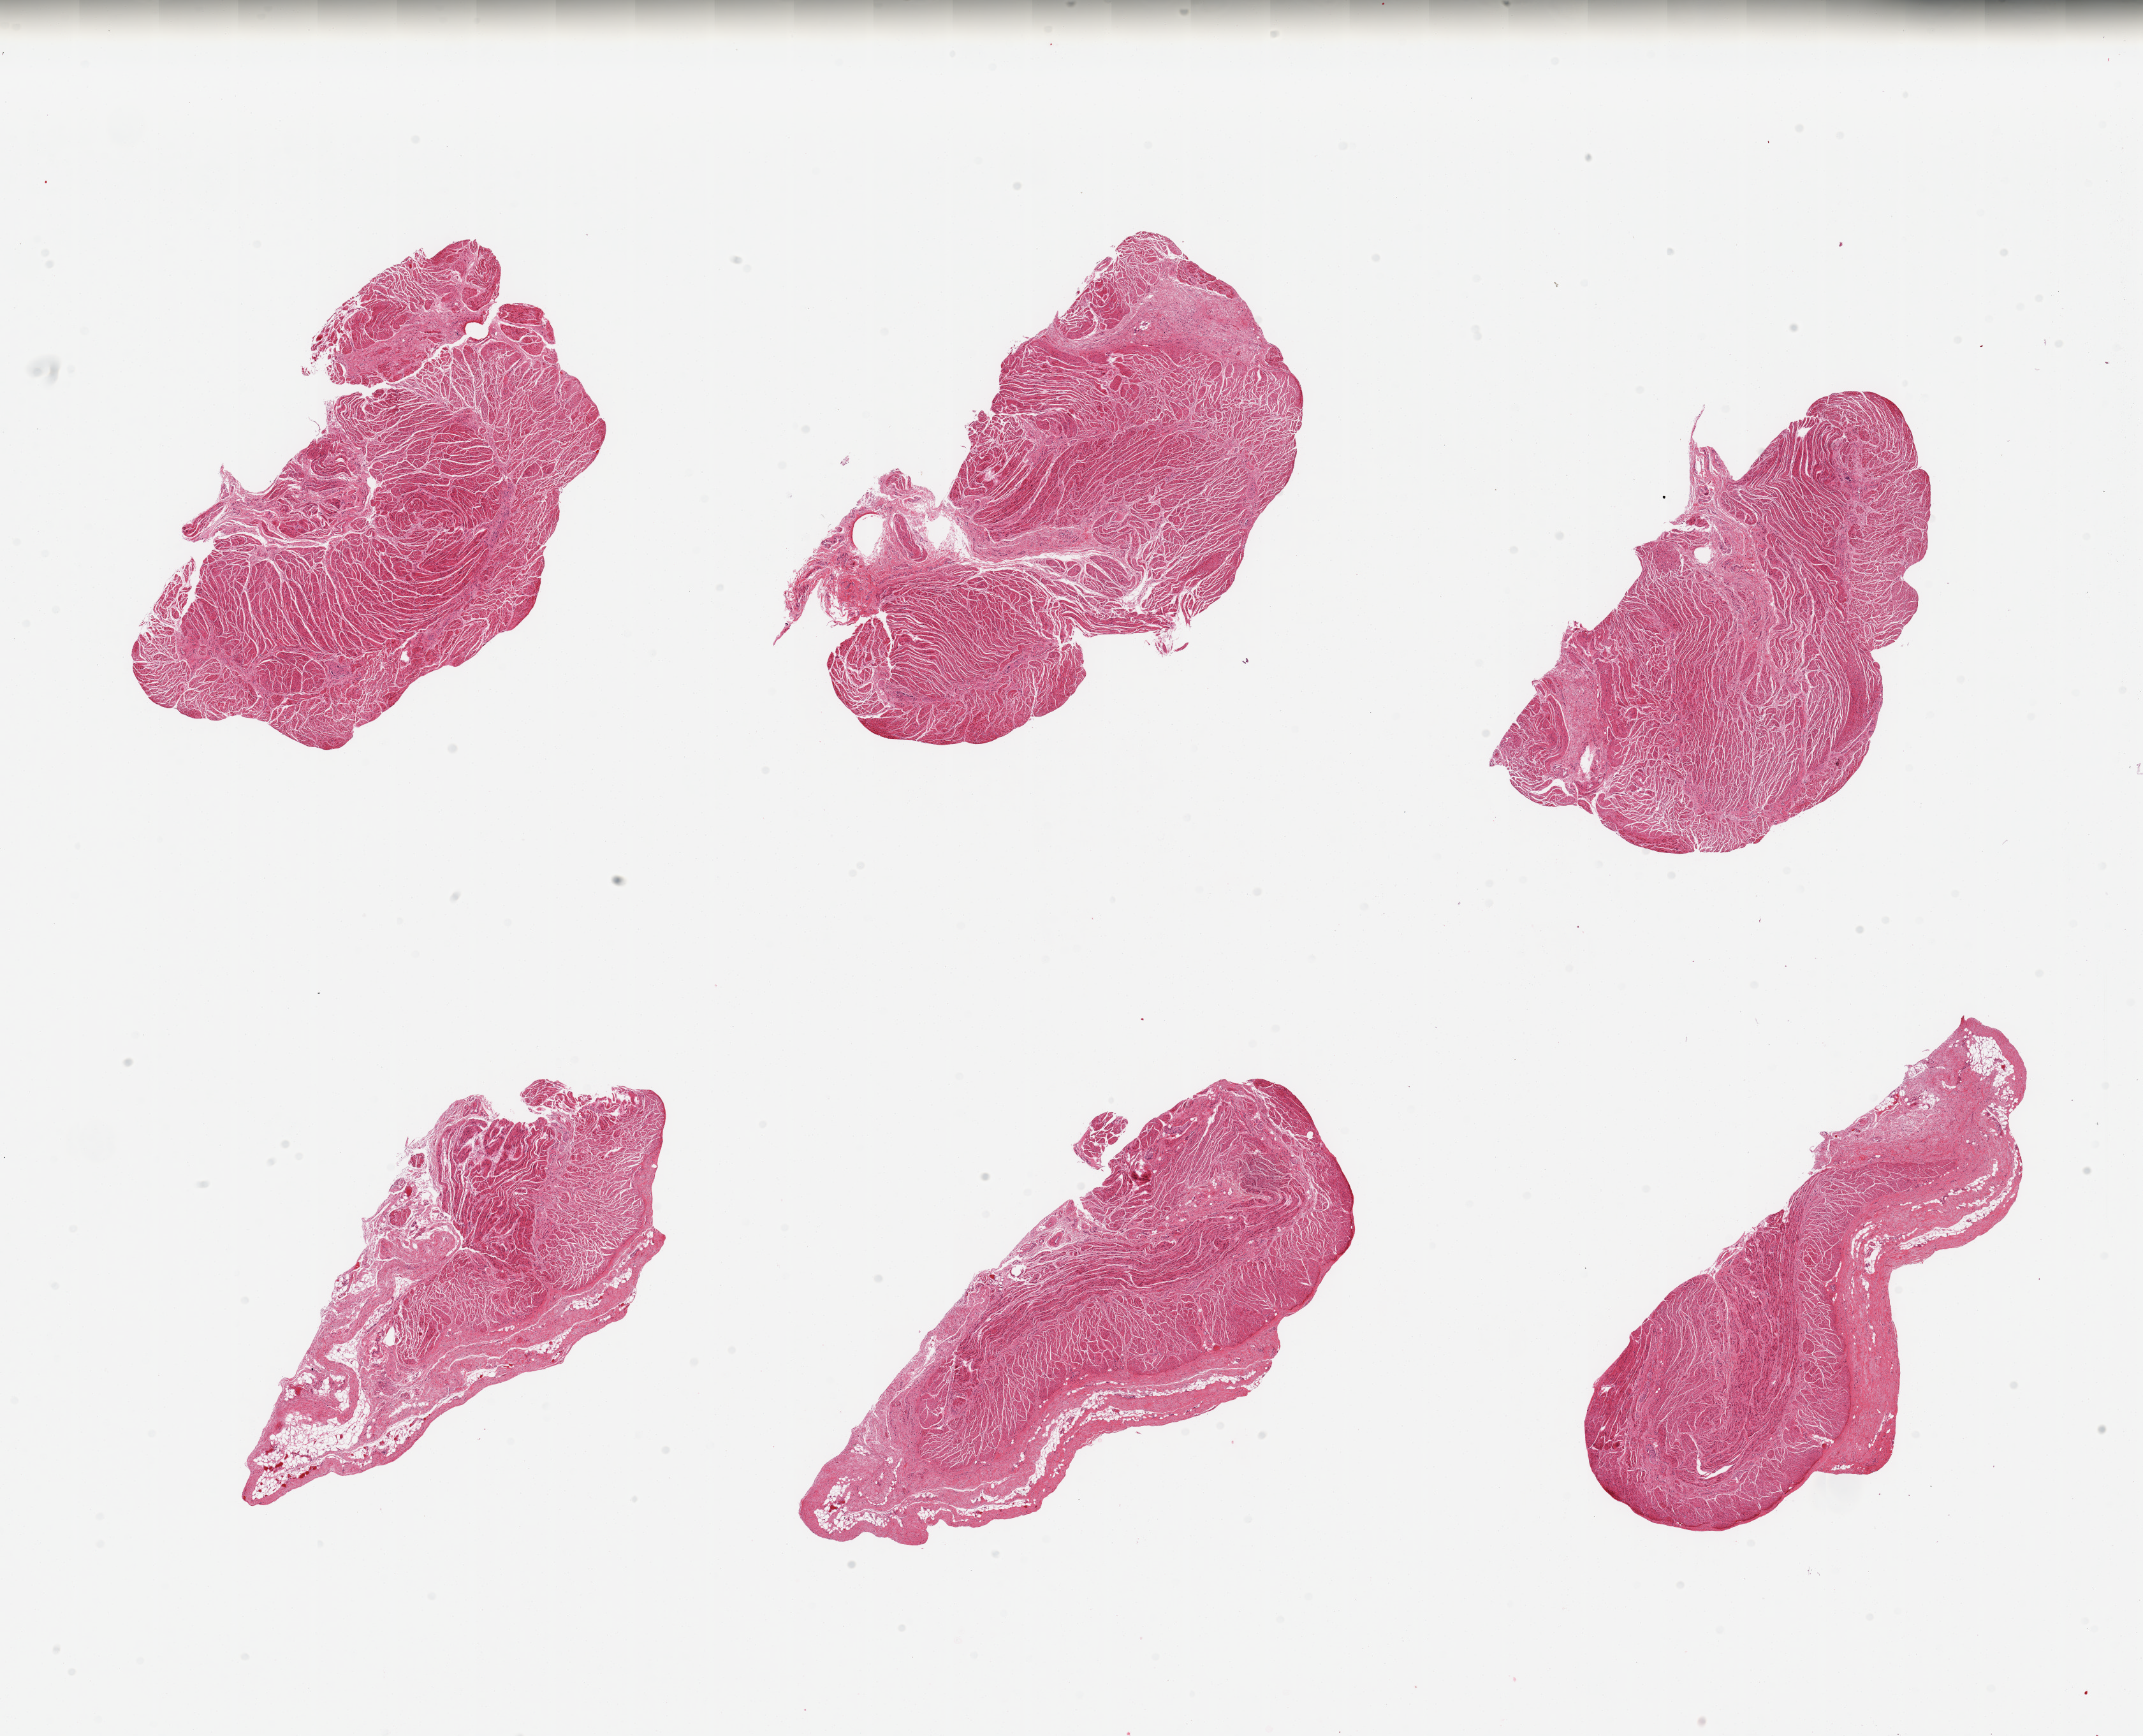
Hematoxylin and eosin (H&E) whole-slide image — low-resolution overview of the scanned area, about 26.6 x 21.5 mm; PAXgene-fixed, paraffin-embedded tissue; section of gastroesophageal junction (target tissue); donor tissue sample. Donor: male.
Pathologist's review note for this sample: 6 pieces; 3 include 20-40% attached fat/connective tissue.